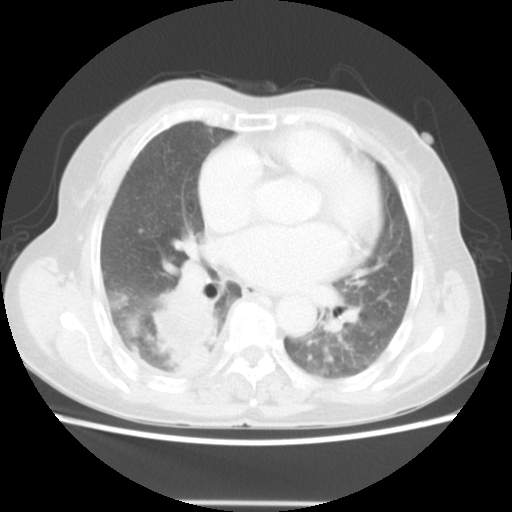
Chest CT, one axial slice. Position 25 of 52 along the scan axis. 140 kVp. Lung window (W 1500 / L -600 HU). 5 mm slice thickness. 512 × 512 image matrix, field of view 337 × 337 mm. Patient: female, 67 years. Case-level facts recorded for this patient, not image findings: clinical TNM (as recorded): T3 N1 M1.
Annotated regions visible in this slice (bounding box drawn by a radiologist):
- lung tumour (recorded histology: adenocarcinoma): box from (x=148, y=290) to (x=216, y=371) px